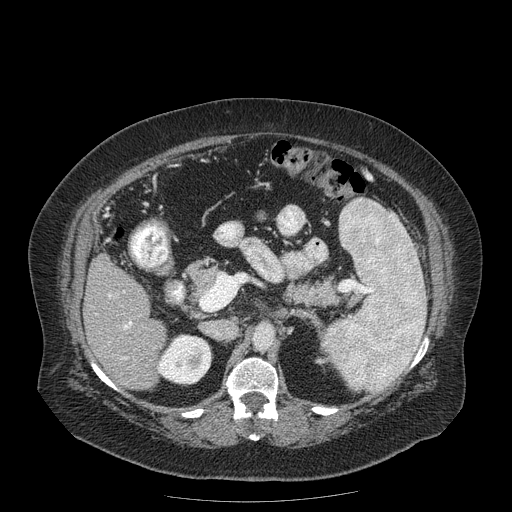
Contrast-enhanced abdominal CT (liver protocol), one axial slice. Reconstruction kernel STANDARD. 120 kVp. Soft-tissue window (W 400 / L 40 HU). 2.5 mm slice thickness. 512 × 512 image matrix. From the clinical record (not read from this slice): diagnosis: hepatocellular carcinoma (patient treated with transarterial chemoembolisation; whether this scan precedes or follows treatment is not stated here); TNM stage (as recorded): Stage-IIIB; Child-Pugh class: A; tumour differentiation: well differentiated; tumour nodularity: uninodular.
Structures marked on this image (semi-automatically segmented with operator editing):
- liver parenchyma outside the tumour (the mass and vessels are separate outlines, so this box may not span the whole liver): bounding box [x1, y1, x2, y2] px = [84, 254, 166, 390]
- liver vessels: [108, 295, 132, 359]